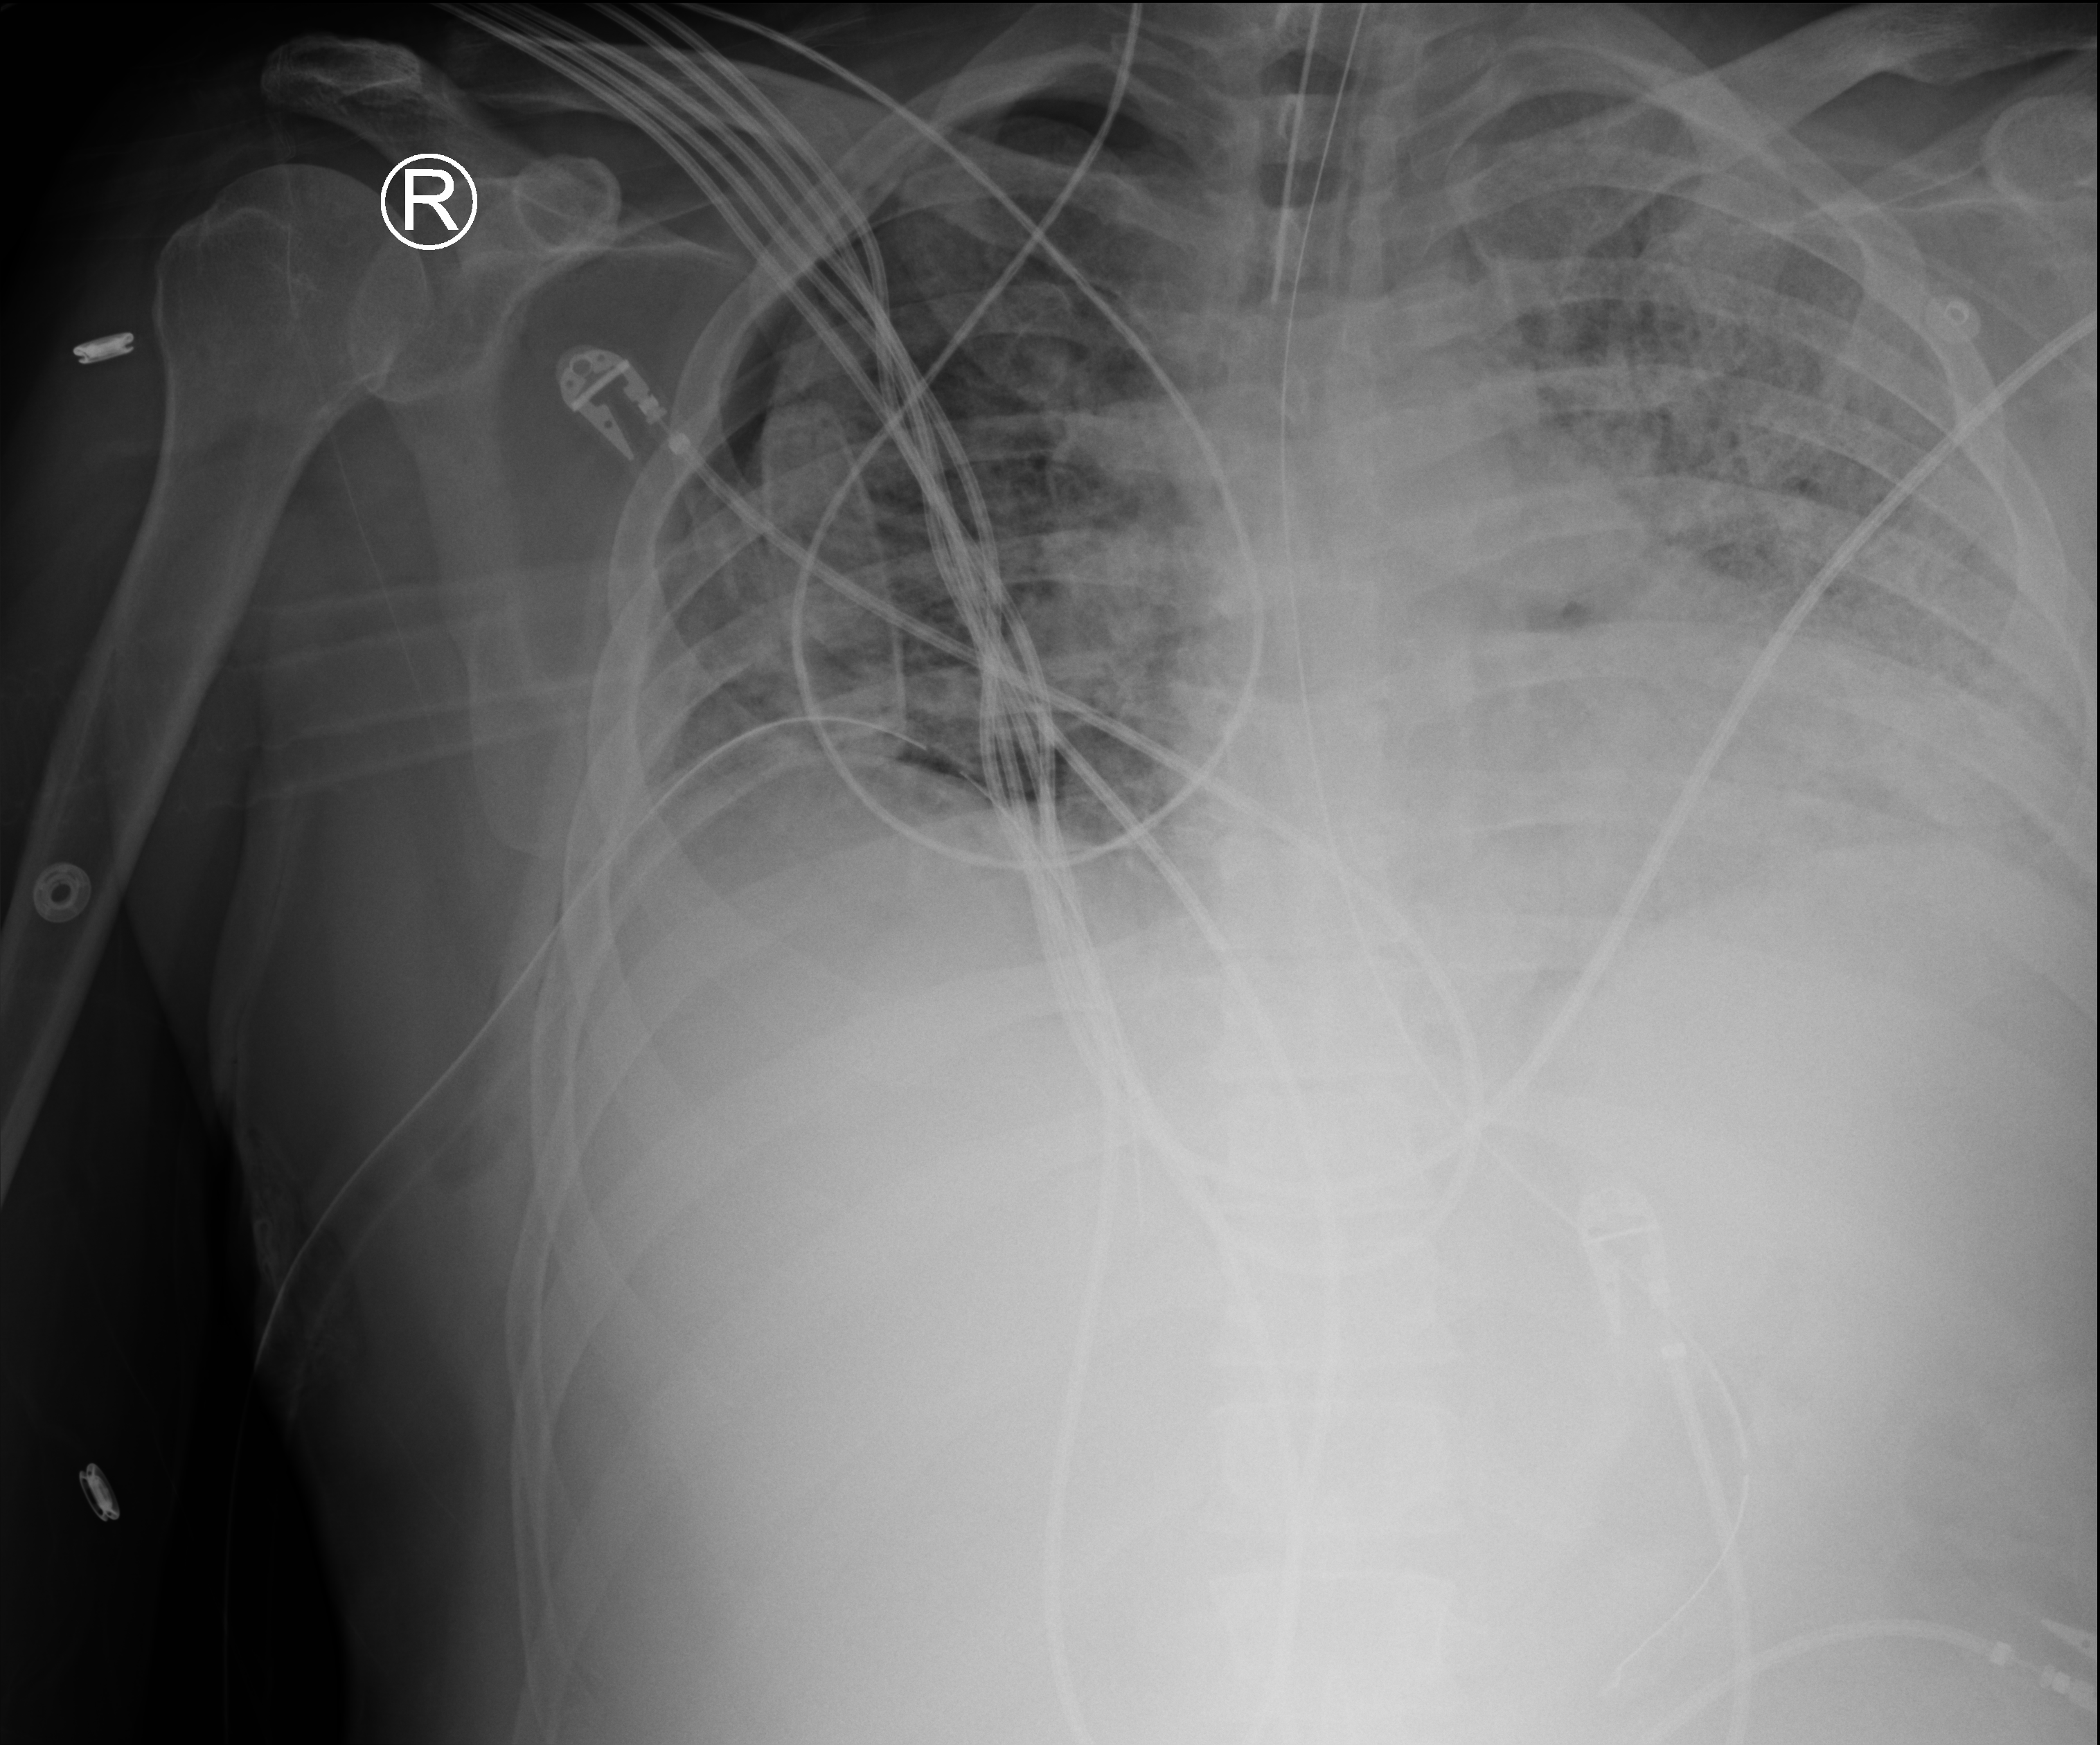
Portable chest radiograph, anteroposterior (AP) projection. Patient hospitalised with COVID-19; male, aged 18–59 years.
Admission-level facts for this patient (not findings on this image; timing relative to this image not recorded): mechanically ventilated during this hospital stay: yes; length of hospital stay: 80 days; diabetes (admission record): no.